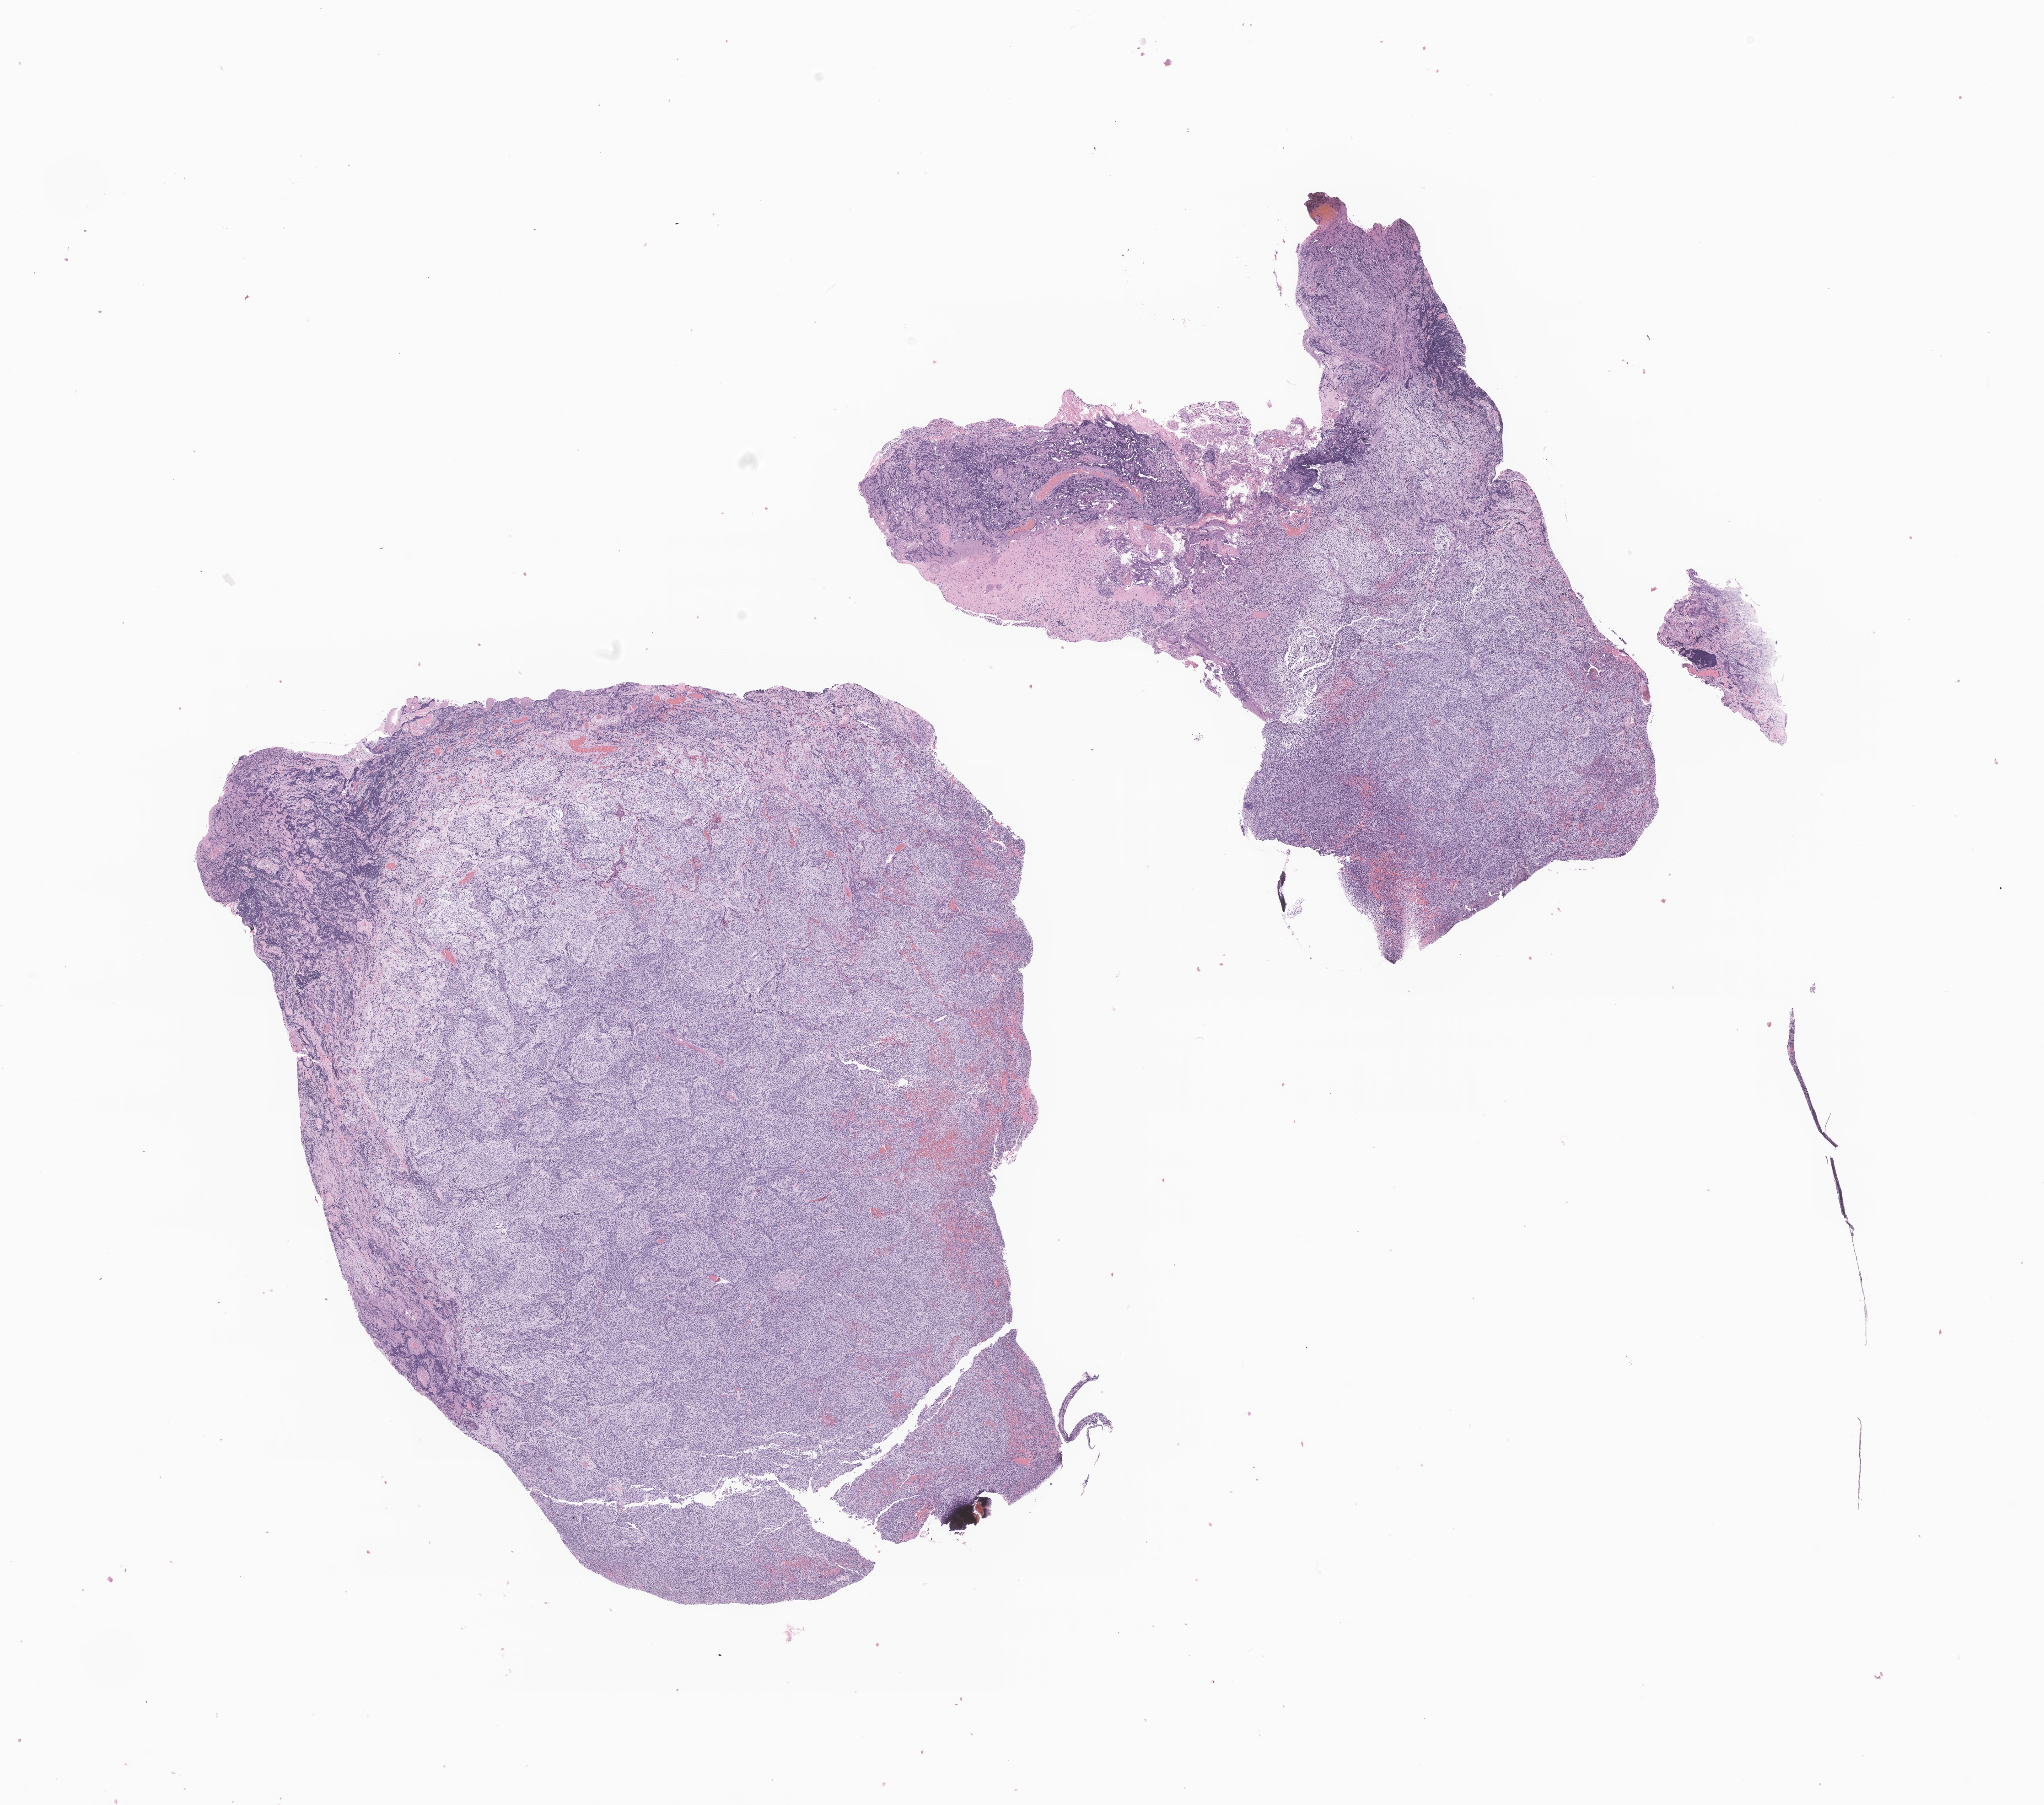
Whole-slide image, hematoxylin and eosin (H&E) stain of tumor tissue from the brain — whole scanned area (about 18.8 x 16.6 mm) shown as a low-resolution overview. FFPE section. Male patient, age 44 months (3 years 8 months).
Recorded diagnosis: Medulloblastoma, NOS.